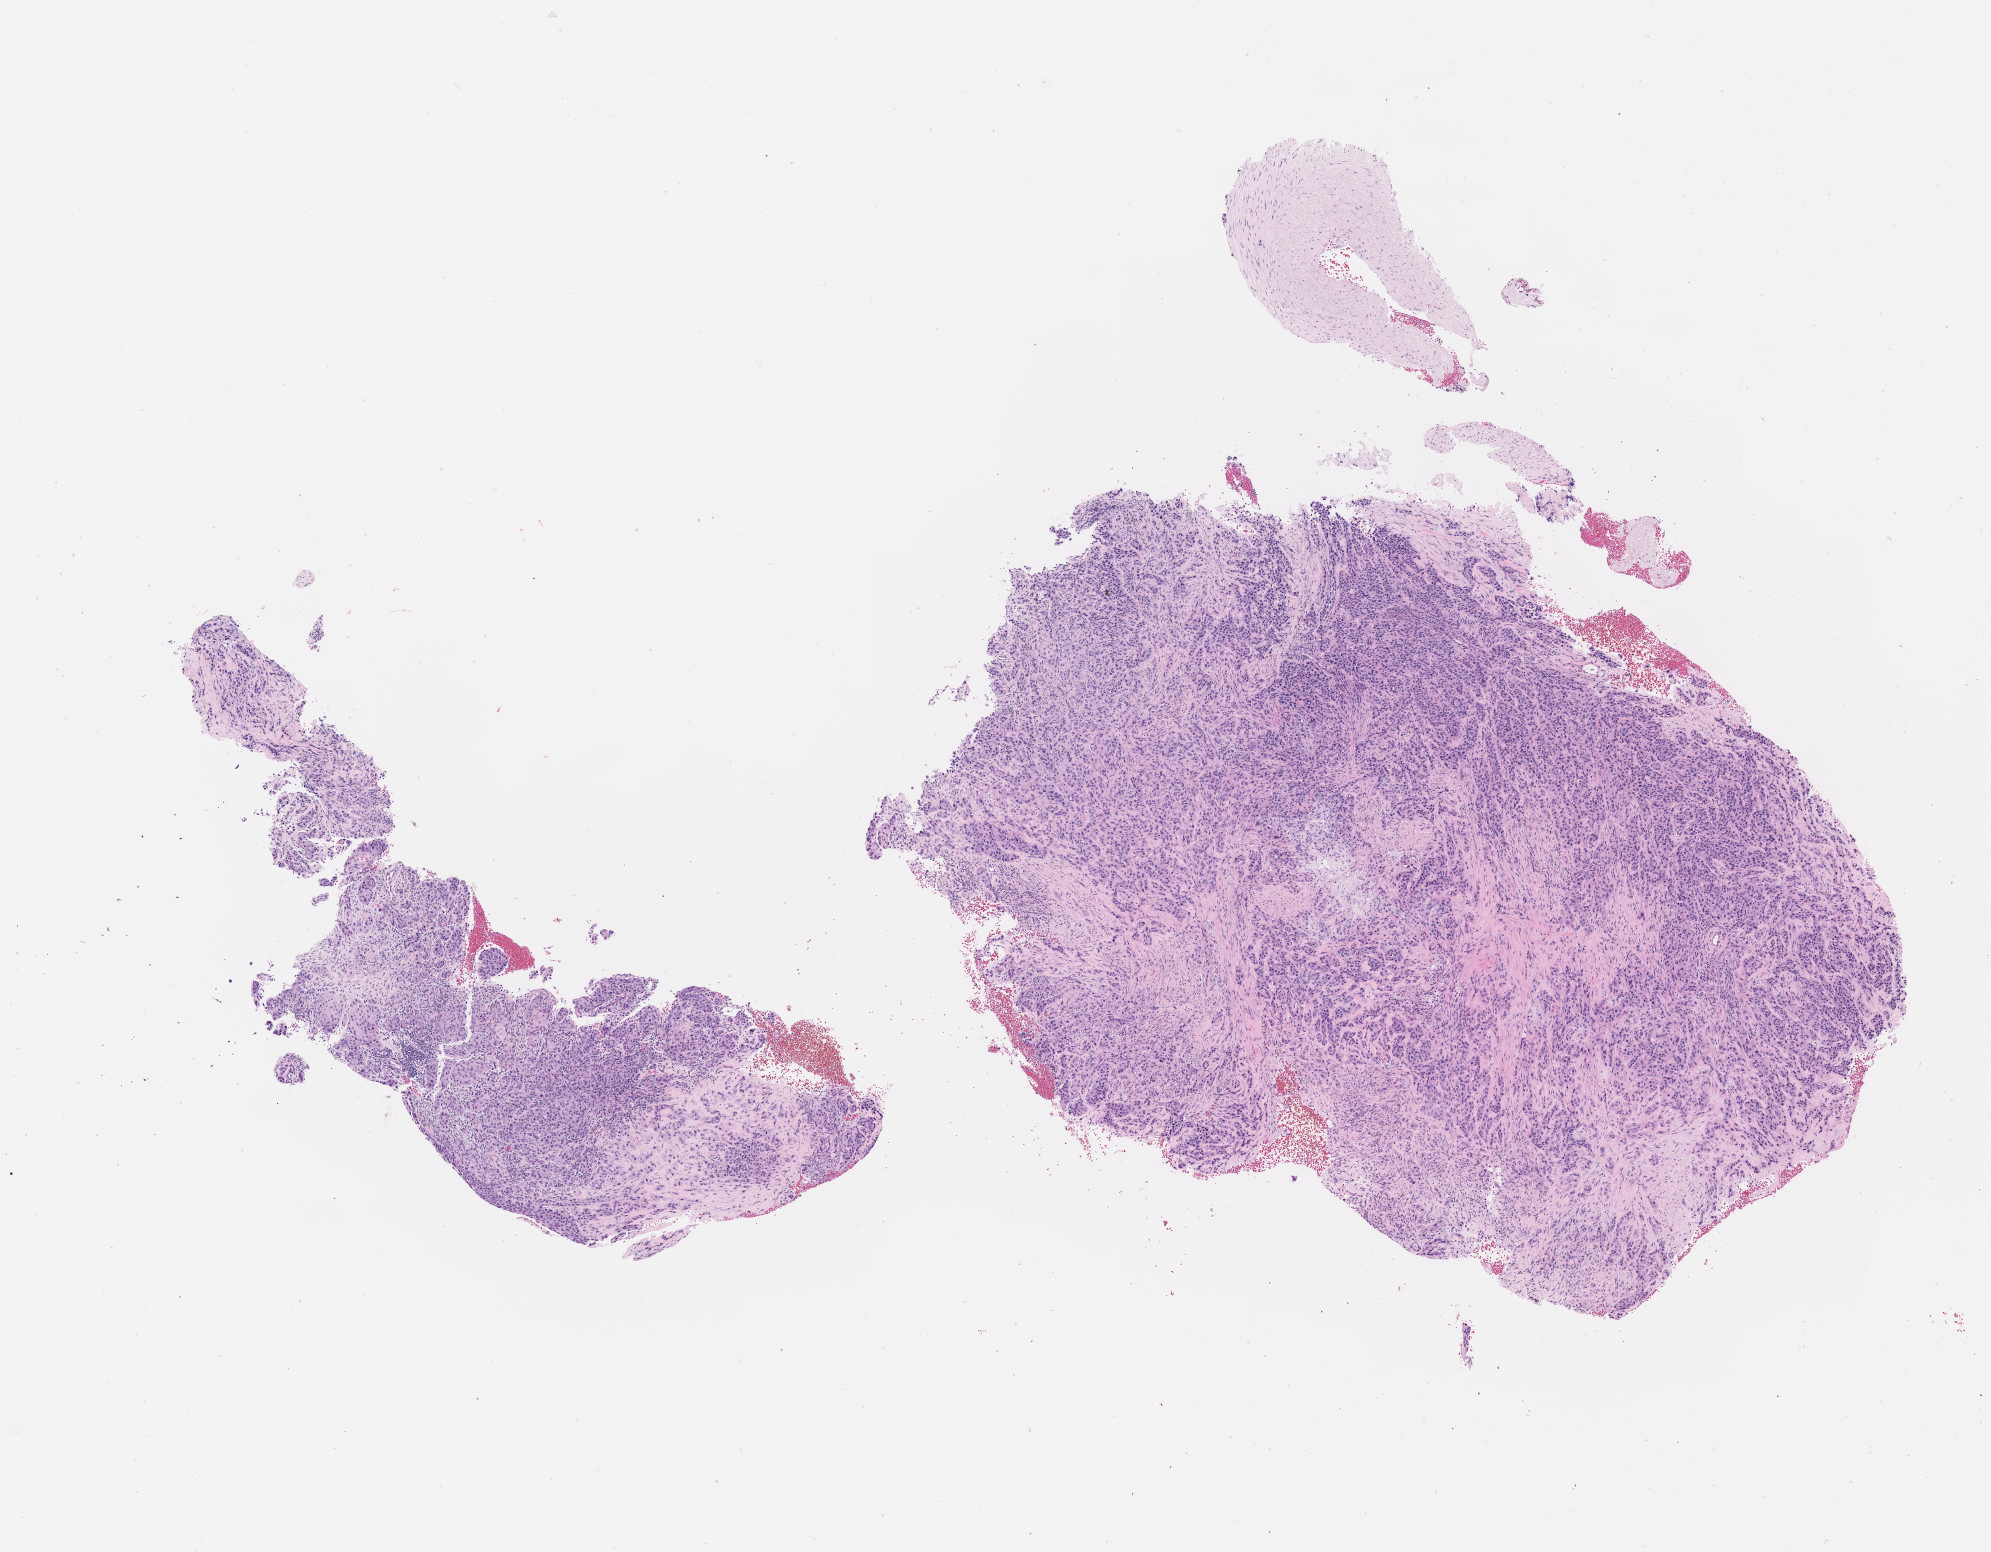
Digitized H&E-stained section, shown as a low-resolution overview of the whole scanned area (about 8.1 x 6.3 mm), tumor tissue, site: cervix. Patient: female, aged 41.
* diagnosis: Squamous cell carcinoma, large cell, nonkeratinizing, NOS